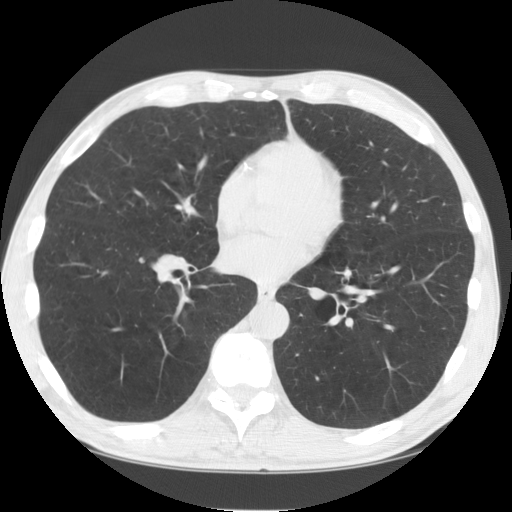
Axial slice from a low-dose chest CT screening exam; first (baseline) screen; lung window (W 1500 / L -600 HU); 2.5 mm slice thickness; slice 90 of 152 in the series; 512 × 512 image matrix. Male participant, aged 60 years at enrolment. Current smoker at enrolment.
Lesion marked by an expert reader, bounding box (x1, y1, x2, y2) in pixels: (123, 241, 161, 274). No non-calcified nodule or mass ≥4 mm was recorded by the screening reader at this exam. Lung cancer was diagnosed 484 days after this screen: large cell carcinoma, NOS, right lower lobe, undifferentiated (G4), stage IA (AJCC 6th edition), 16 mm at pathology.